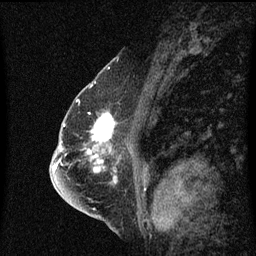
Breast MRI (dynamic contrast-enhanced), one sagittal slice. Slice 39 of 60 in the series (ordered by position). Dynamic contrast-enhanced series, image 2 of 3 at this slice position (ordered by acquisition). 1.5 T. TE 4.2 ms, TR 8.4 ms. 2 mm slice thickness. 256 × 256 image matrix, field of view 200 × 200 mm. Patient: female, 57 years. From the clinical record (not read from this slice): setting: breast cancer imaged before/during neoadjuvant chemotherapy; receptor status: HR-positive, HER2-negative.
Outlined on this slice (semi-automatic segmentation, software-assisted and operator-edited):
- analysis volume of interest (the breast-tissue region the enhancement analysis was run in; not a lesion): bounding box <92,112,116,145> (left, top, right, bottom; pixels)
- tumour enhancement mask (voxels above the 70 % enhancement threshold inside the analysis volume of interest): <93,116,115,143>